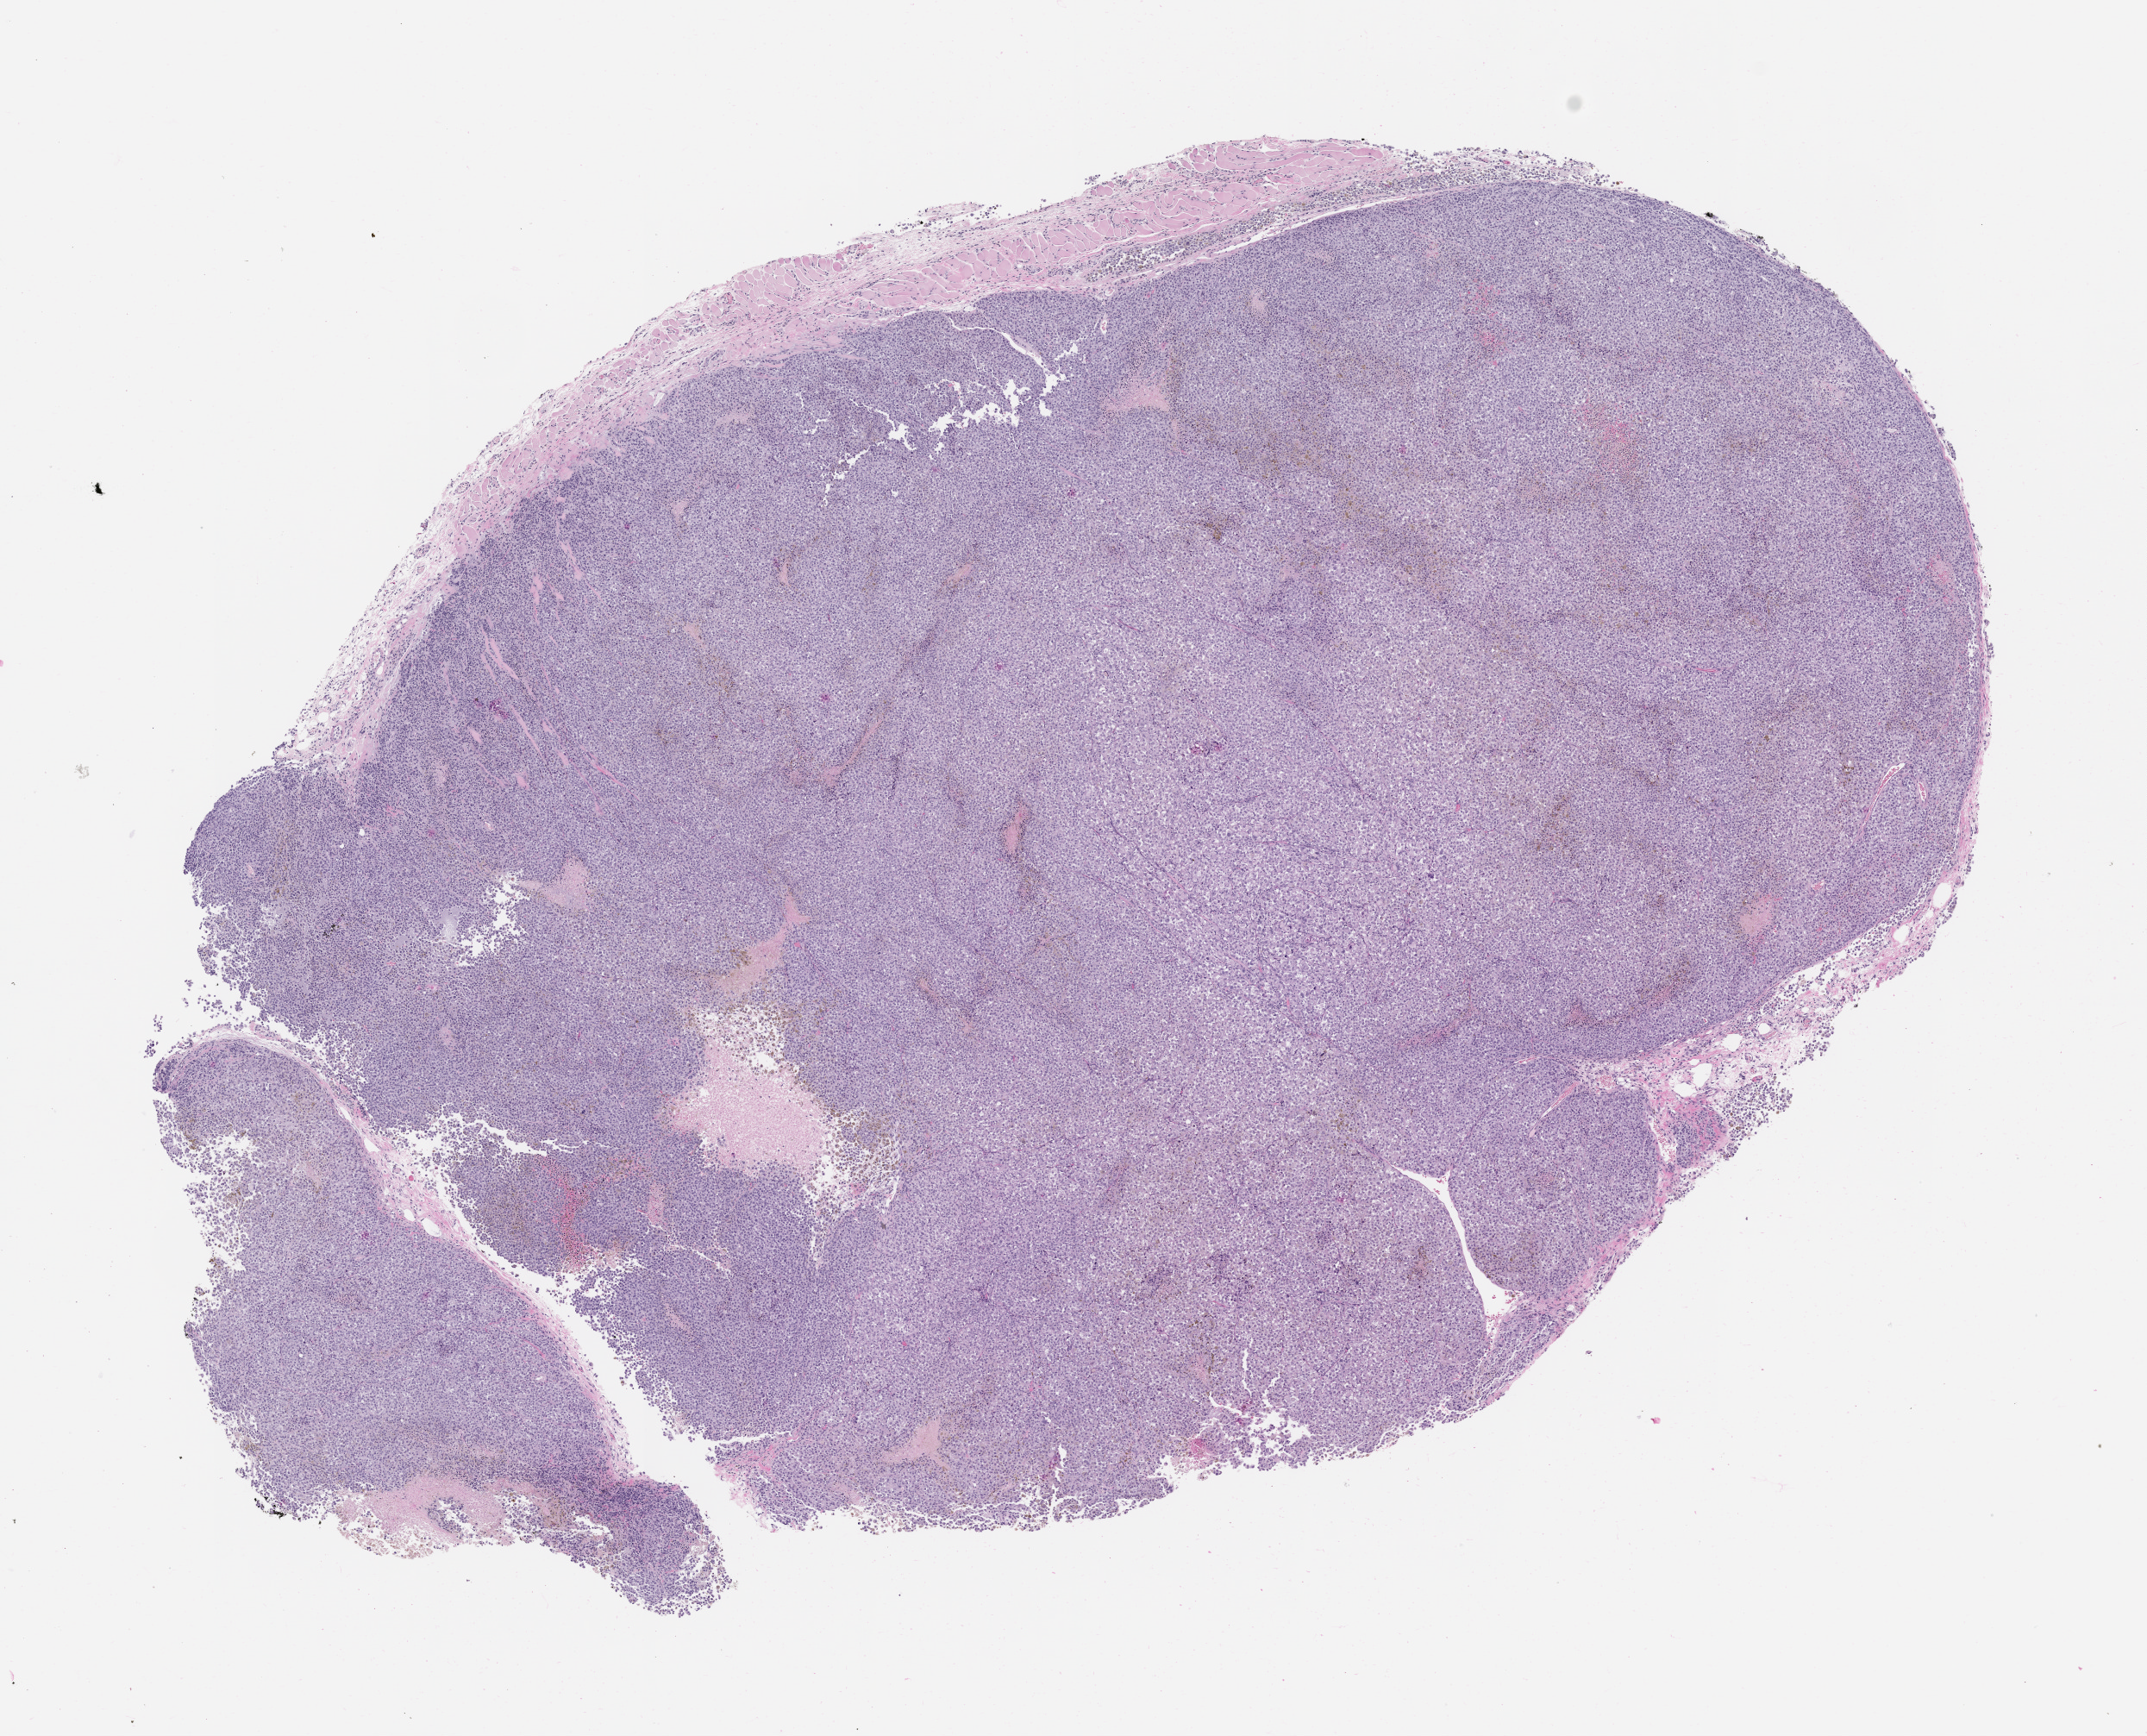
Hematoxylin and eosin (H&E) whole-slide image of a patient-derived xenograft (PDX) tumor grown in a mouse, passage 1 — whole scanned area (about 10.0 x 8.1 mm) shown as a low-resolution overview, formalin-fixed paraffin-embedded section, originating tumor site category: skin.
Originating patient diagnosis: Melanoma.